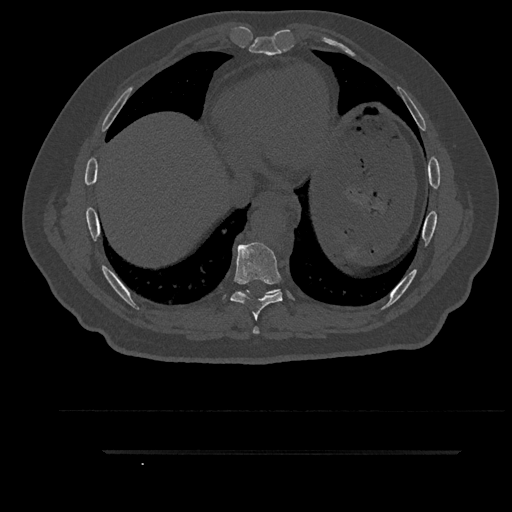
CT including the spine, one axial slice. Reconstruction kernel Br40s/3. 120 kVp. Bone window (W 1800 / L 400 HU). 0.5 mm slice thickness. 512 × 512 image matrix, field of view 432 × 432 mm. Patient: male, 63 years. Case-level facts recorded for this patient, not image findings: primary cancer: renal.
Annotated regions visible in this slice (semi-automatic segmentation, software-assisted and operator-edited):
- T7 vertebra: bounding box <253,326,259,334> (left, top, right, bottom; pixels)
- T8 vertebra: <231,242,282,320>
- T9 vertebra: <245,290,279,295>